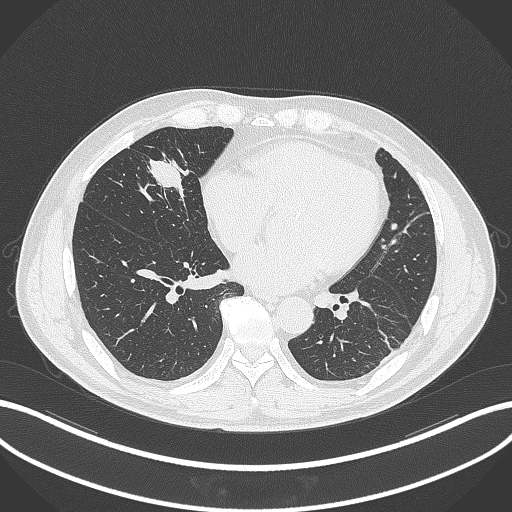
Chest CT, one axial slice. Slice 107 of 399 in the series (ordered by position). Reconstruction kernel B70f. 120 kVp. Lung window (W 1500 / L -600 HU). 1 mm slice thickness. 512 × 512 image matrix, field of view 400 × 400 mm. Male patient, age 59 years. Case-level facts recorded for this patient, not image findings: clinical TNM (as recorded): T2a N1 M0.
Outlined on this slice (bounding box drawn by a radiologist):
- lung tumour (recorded histology: adenocarcinoma): box from (x=144, y=153) to (x=194, y=201) px